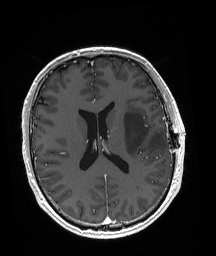
Brain MRI from a brain-tumour surgery series, one axial slice; slice 84 of 192 in the series (ordered by position); T1-weighted post-contrast; 216 × 256 image matrix. Case-level facts recorded for this patient, not image findings: histopathology: Astrocytoma; WHO grade: 3; IDH mutation: yes; tumour location: Left Posterior Frontal.
Structures marked on this image (expert manual segmentation):
- tumour: bounding box (x1, y1, x2, y2) in pixels: (123, 111, 167, 156)